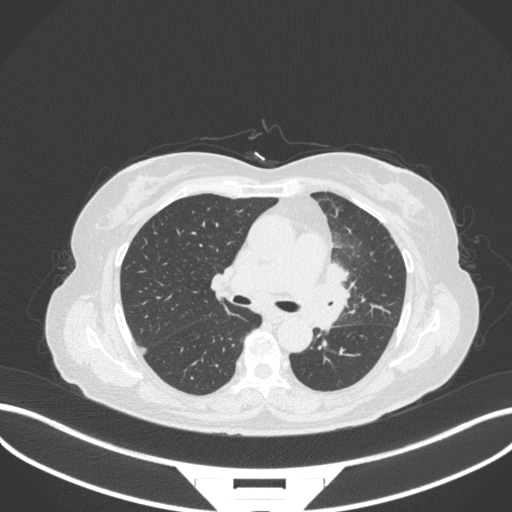
Chest CT, one axial slice. Position 200 of 382 along the scan axis. Reconstruction kernel B31f. 120 kVp. Lung window (W 1500 / L -600 HU). 512 × 512 image matrix. Female patient, age 64 years. From the clinical record (not read from this slice): clinical TNM (as recorded): T2a N2 M0.
Annotated regions visible in this slice (bounding box drawn by a radiologist):
- lung tumour (recorded histology: adenocarcinoma): box from (x=314, y=256) to (x=357, y=331) px